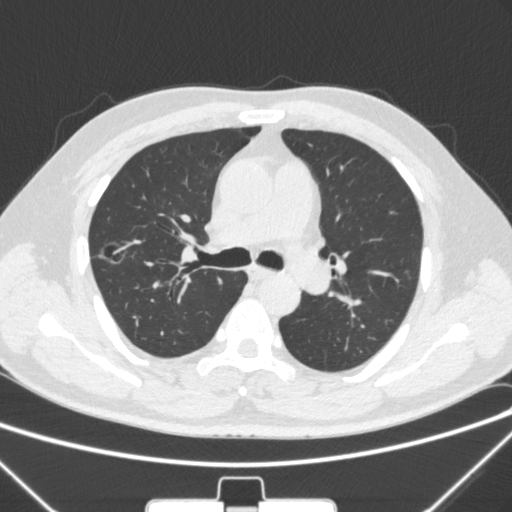
Chest CT, one axial slice; position 196 of 320 along the scan axis; lung window (W 1500 / L -600 HU); 512 × 512 image matrix. Male patient, age 58 years. Case-level facts recorded for this patient, not image findings: clinical TNM (as recorded): T1c N0 M0; histopathological grade: G2.
Outlined on this slice (bounding box drawn by a radiologist):
- lung tumour (recorded histology: adenocarcinoma): box from (x=98, y=236) to (x=132, y=267) px